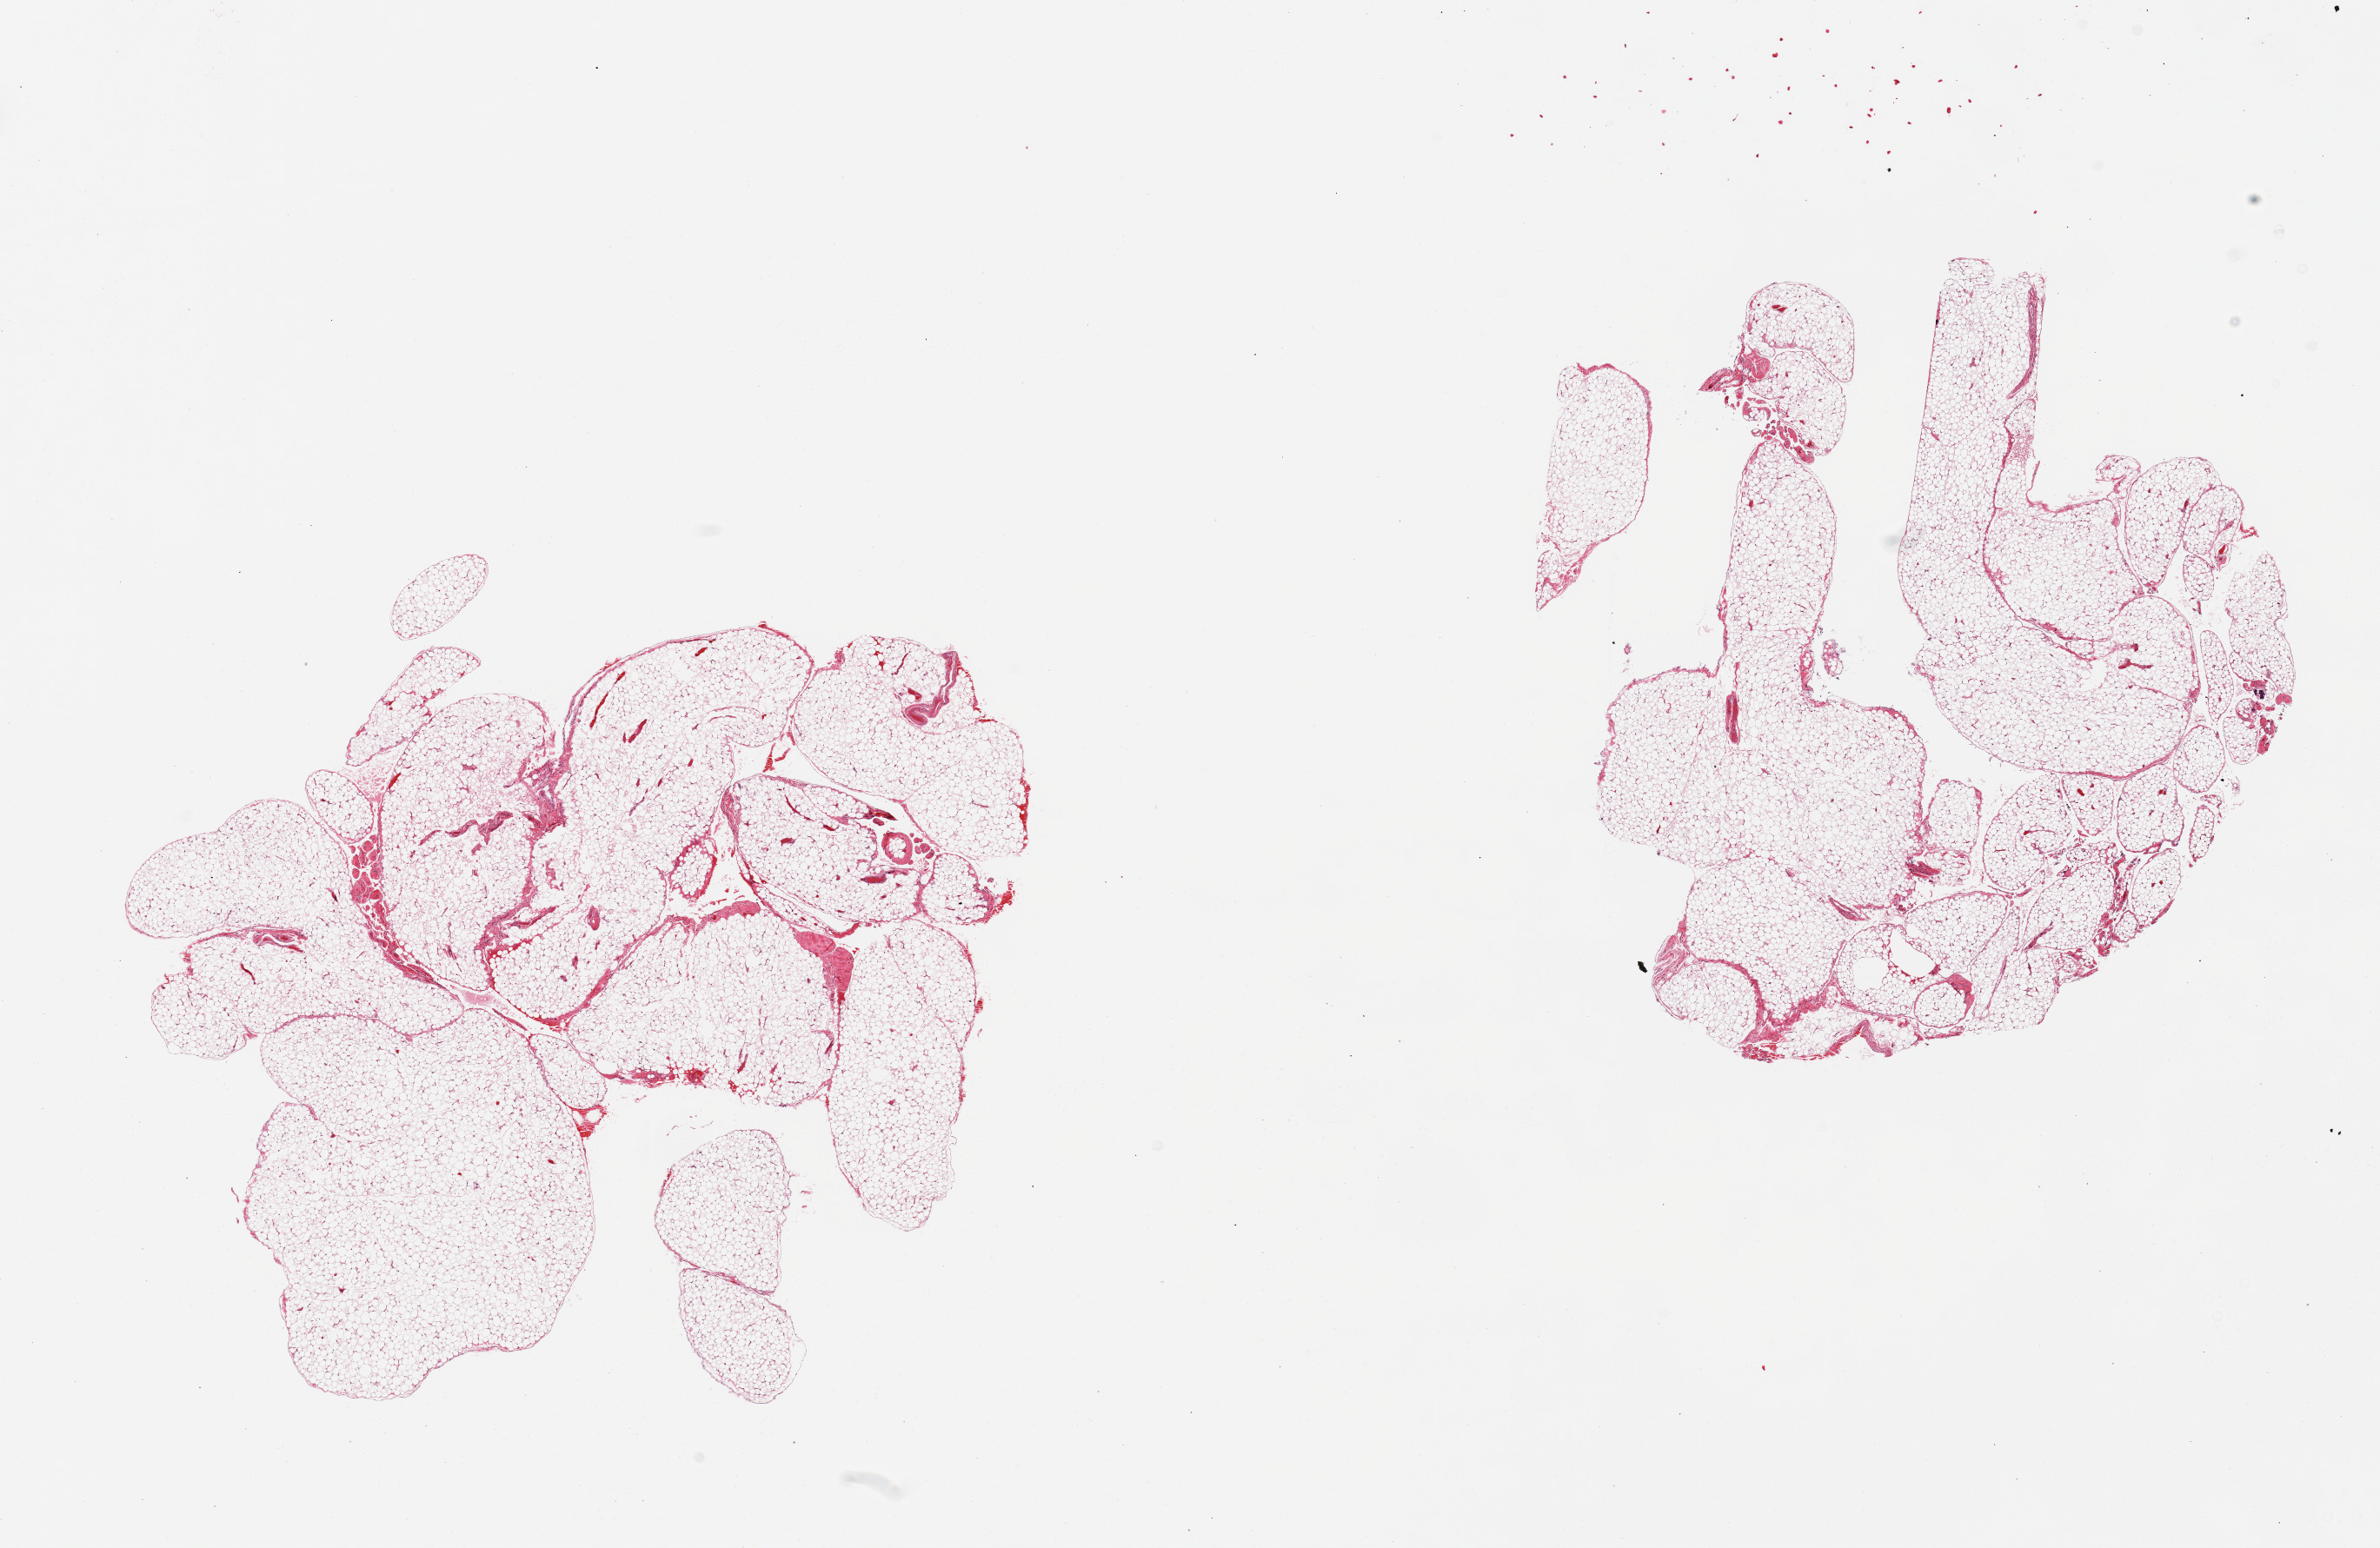
Whole-slide image, hematoxylin and eosin (H&E) stain — a low-resolution overview of the entire scanned area, about 21.7 x 14.1 mm, PAXgene-fixed paraffin-embedded (PFPE) section, target tissue: omentum, tissue donor sample. Female donor.
- reviewer comment on this tissue sample: 2 pieces; minimal fibrovascular component